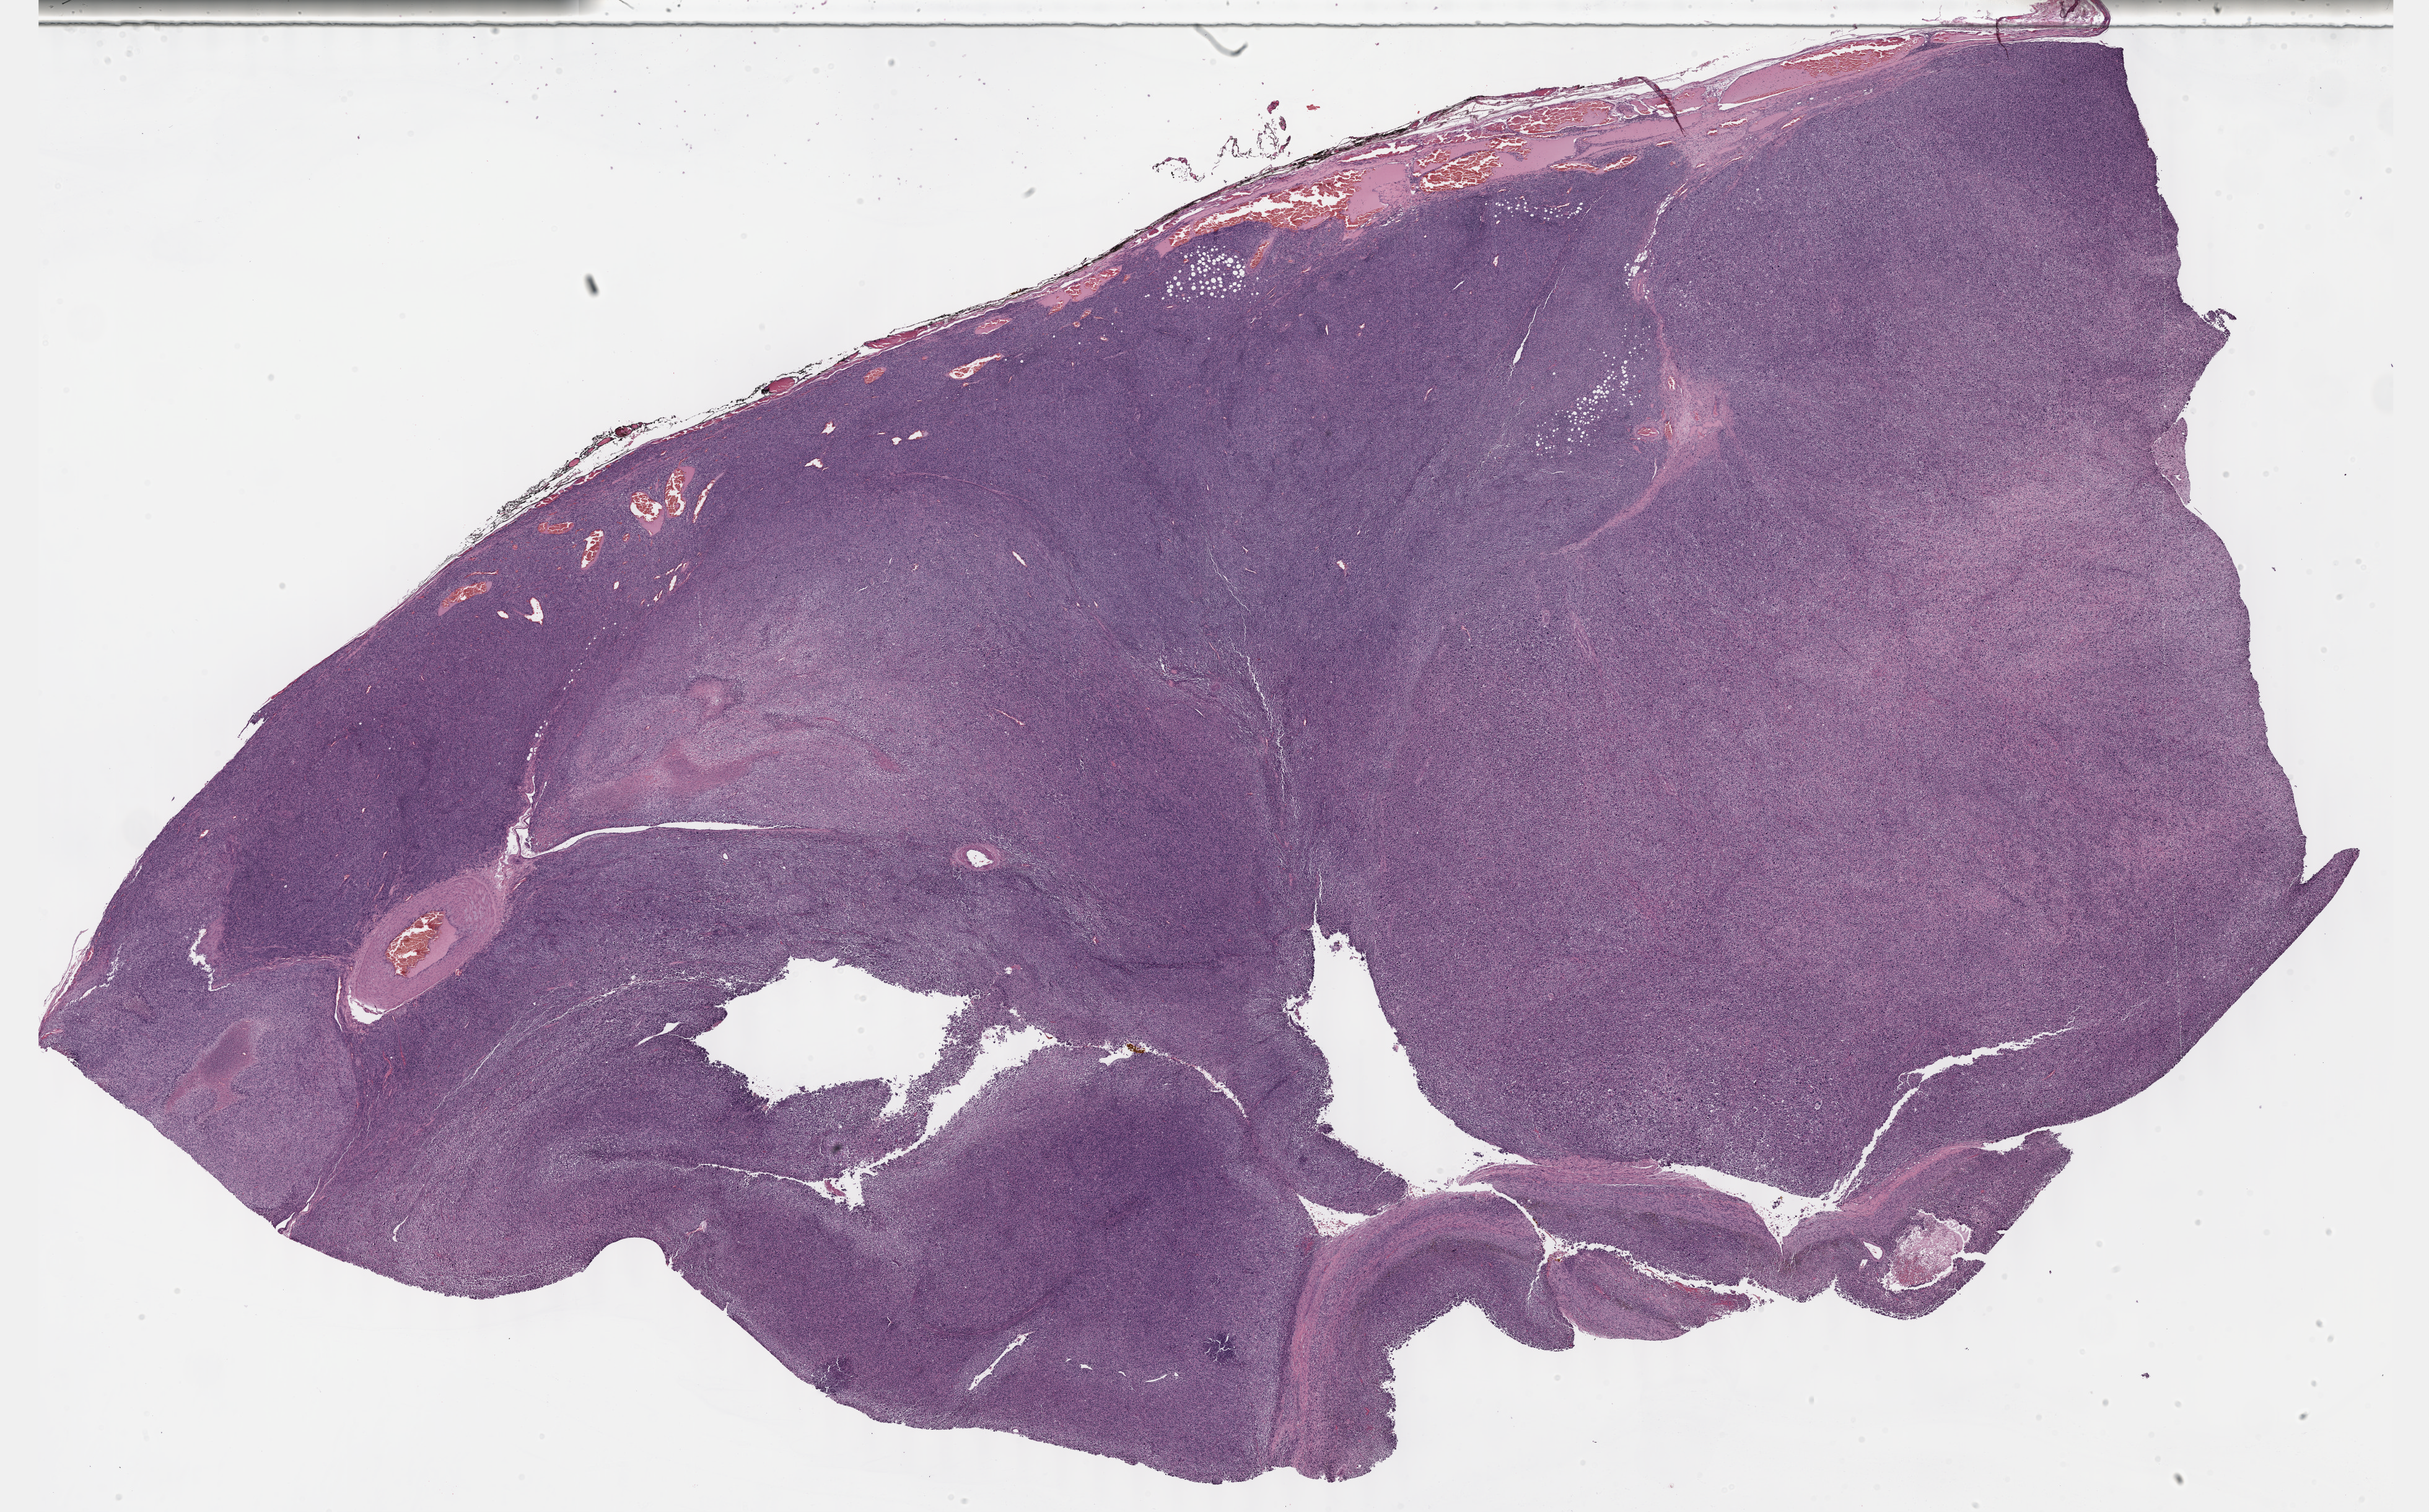
Digitized Hematoxylin and eosin (H&E) stained tissue section (whole slide) — a low-resolution overview of the entire scanned area, about 31.7 x 19.7 mm (from a 40x scan). Formalin-fixed paraffin-embedded (FFPE) diagnostic section. Sample: primary tumour, connective, subcutaneous and other soft tissues. Patient: male, age at initial diagnosis 29 years.
- pathologic diagnosis: Malignant peripheral nerve sheath tumor (connective, subcutaneous and other soft tissues of lower limb and hip)